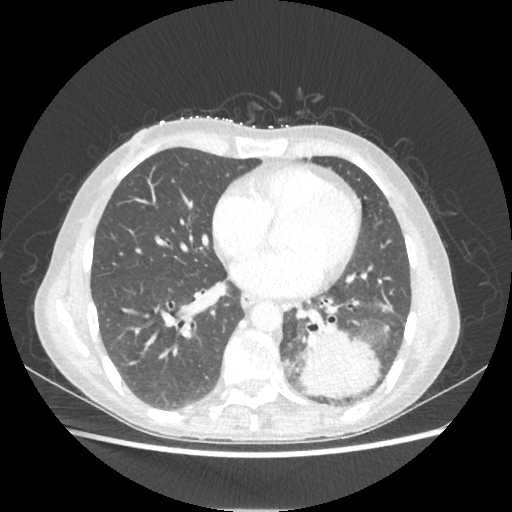
Chest CT, one axial slice; slice 93 of 221 in the series (ordered by position); 80 kVp; lung window (W 1500 / L -600 HU); 1.25 mm slice thickness; 512 × 512 image matrix, field of view 360 × 360 mm. Patient: female, 53 years. From the clinical record (not read from this slice): clinical TNM (as recorded): T3 N0 M0.
Structures marked on this image (rectangle marked by the reading radiologist):
- lung tumour (recorded histology: adenocarcinoma): bounding box <296,321,383,398> (left, top, right, bottom; pixels)